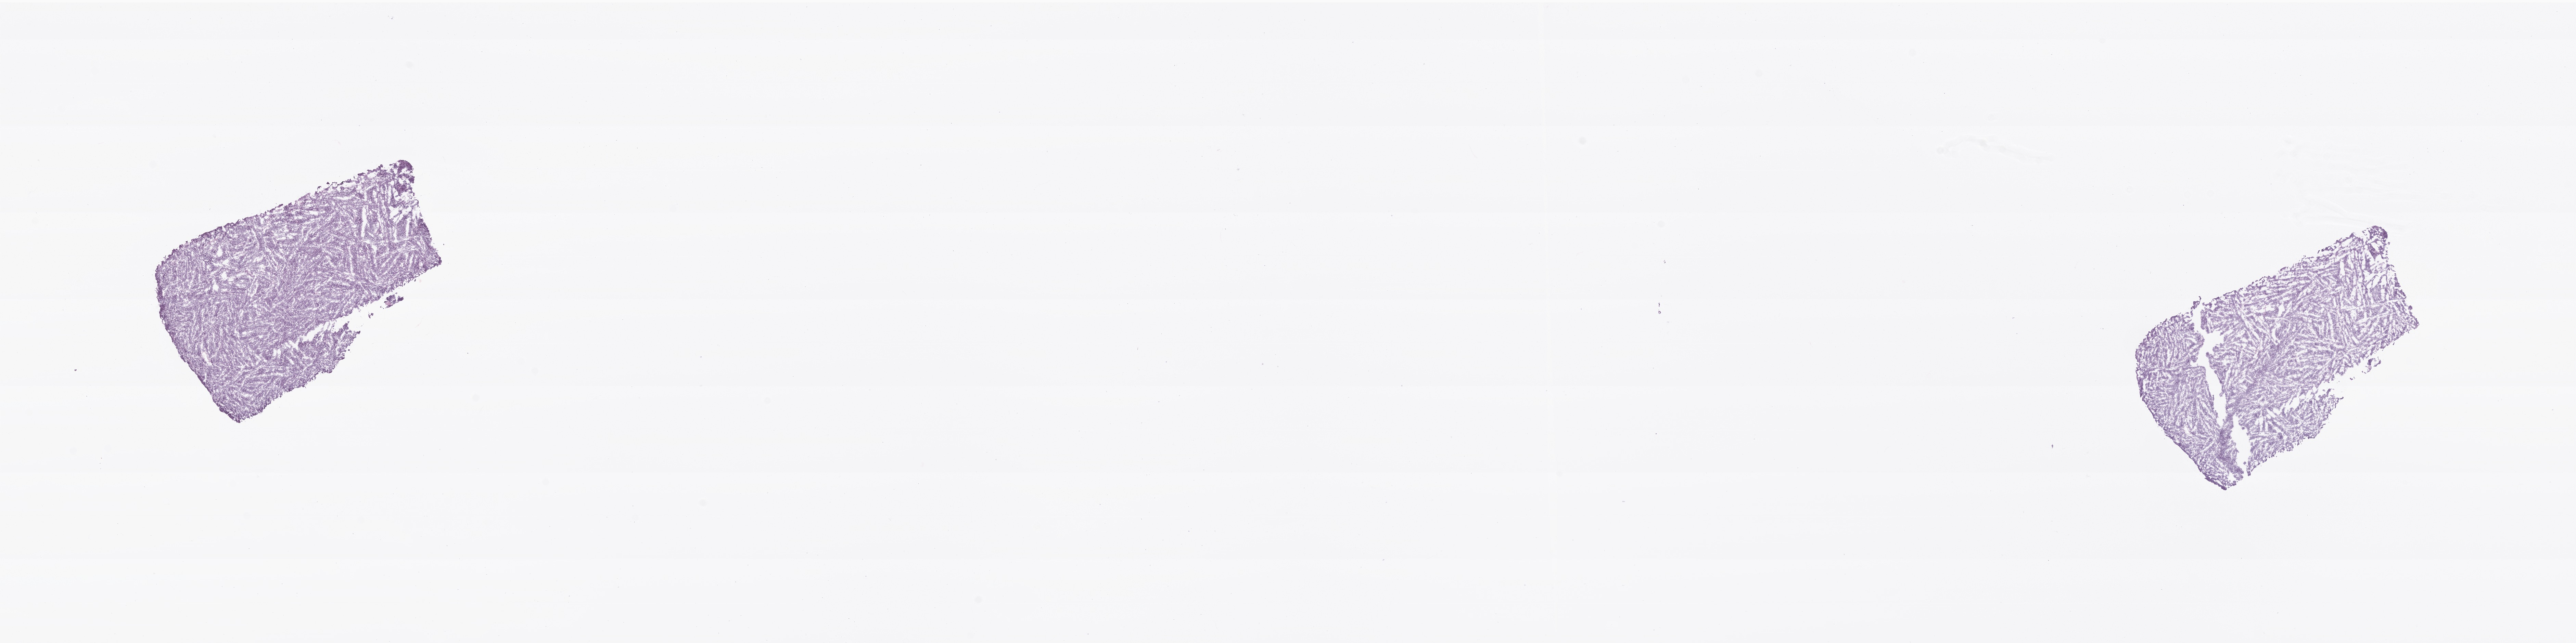
Whole-slide image, haematoxylin and eosin stain of tumor tissue from the brain, low-resolution overview of the scanned area, about 31.6 x 7.9 mm, frozen section. Male patient, age 183 months (15 years 3 months).
Recorded diagnosis: Neoplasm, uncertain whether benign or malignant.